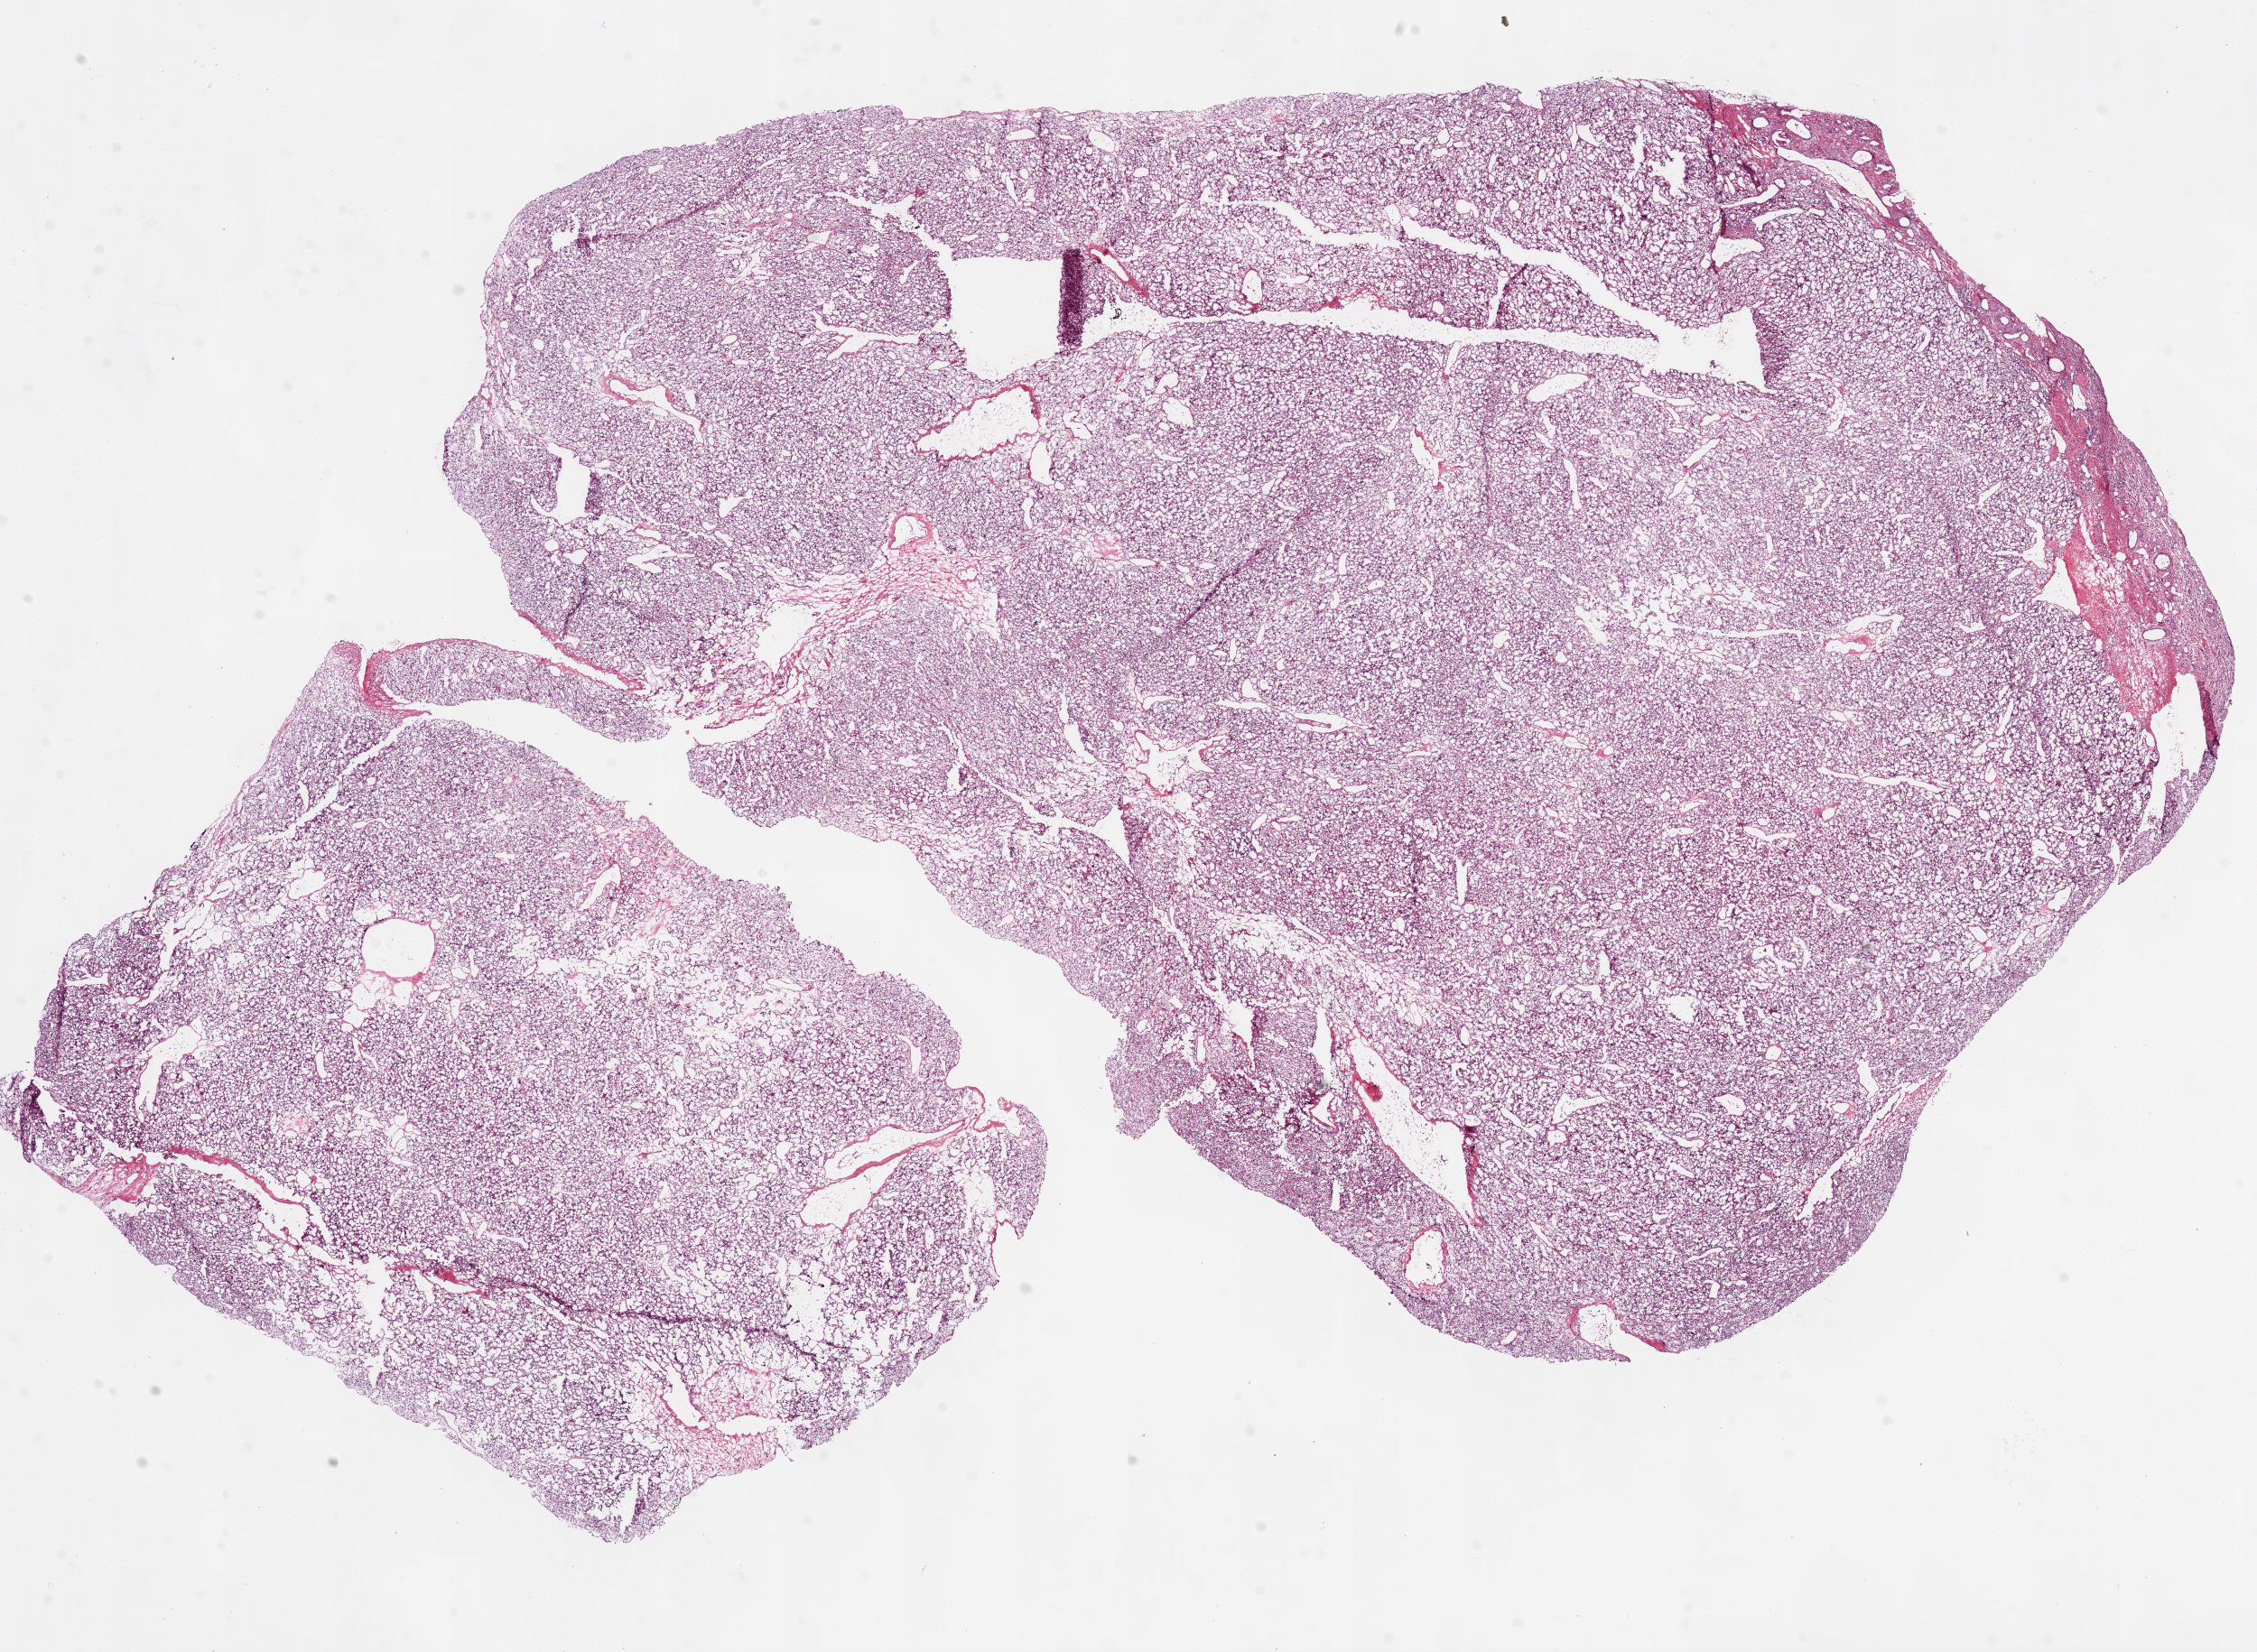
H&E-stained whole-slide image, shown as a low-resolution overview of the whole scanned area (about 20.1 x 14.7 mm, slide scanned at 20x). Frozen section from the bottom of the tissue portion. Kidney, primary tumour sample. Male patient; age at initial diagnosis 40 years. Histologic grade: G2 (moderately differentiated). Slide review estimates, as recorded: tumour cells 95%, tumour nuclei 95%, stromal cells 5%, necrosis 0%. Inflammatory infiltration, as recorded: lymphocyte infiltration 1%.
Laterality: right. AJCC pathologic stage: I. Histologic diagnosis: Clear cell adenocarcinoma, NOS.